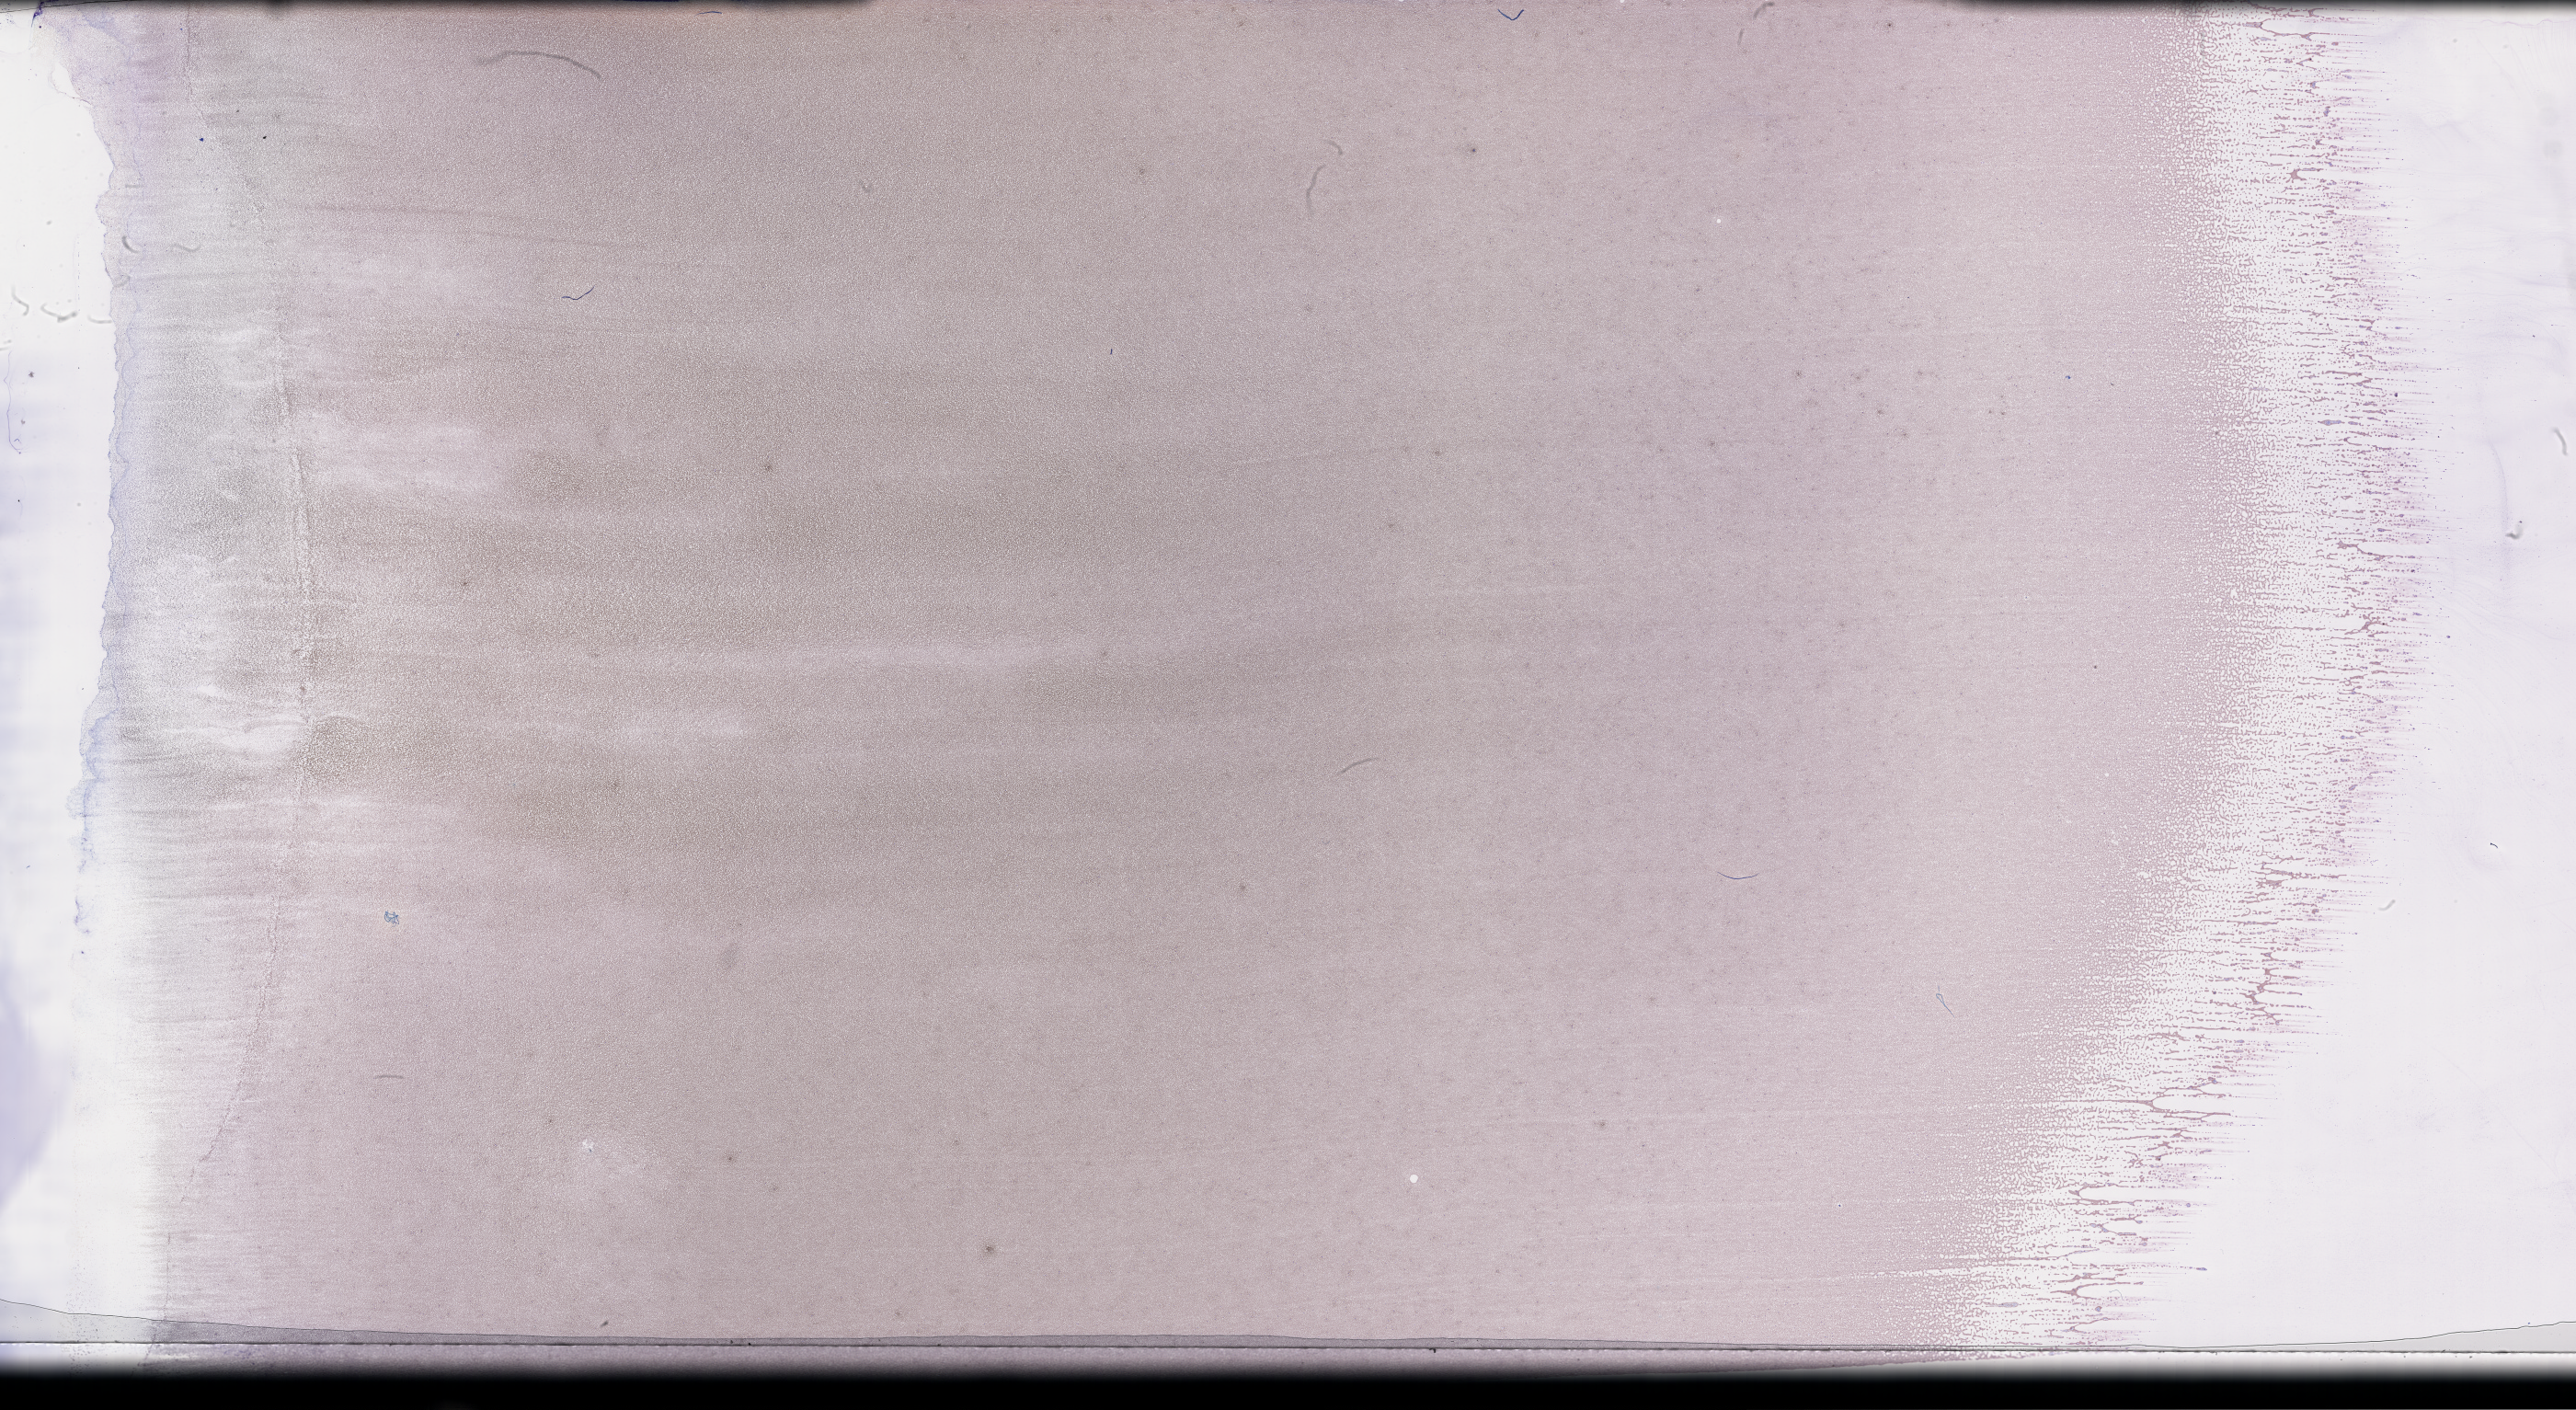
Wright–Giemsa-stained whole blood smear, whole-slide image — a low-resolution overview of the entire scanned area, about 45.2 x 24.8 mm; smear from an EDTA sample; specimen time point: collected on treatment. Patient: female.
• from a patient with: Plasma Cell Myeloma